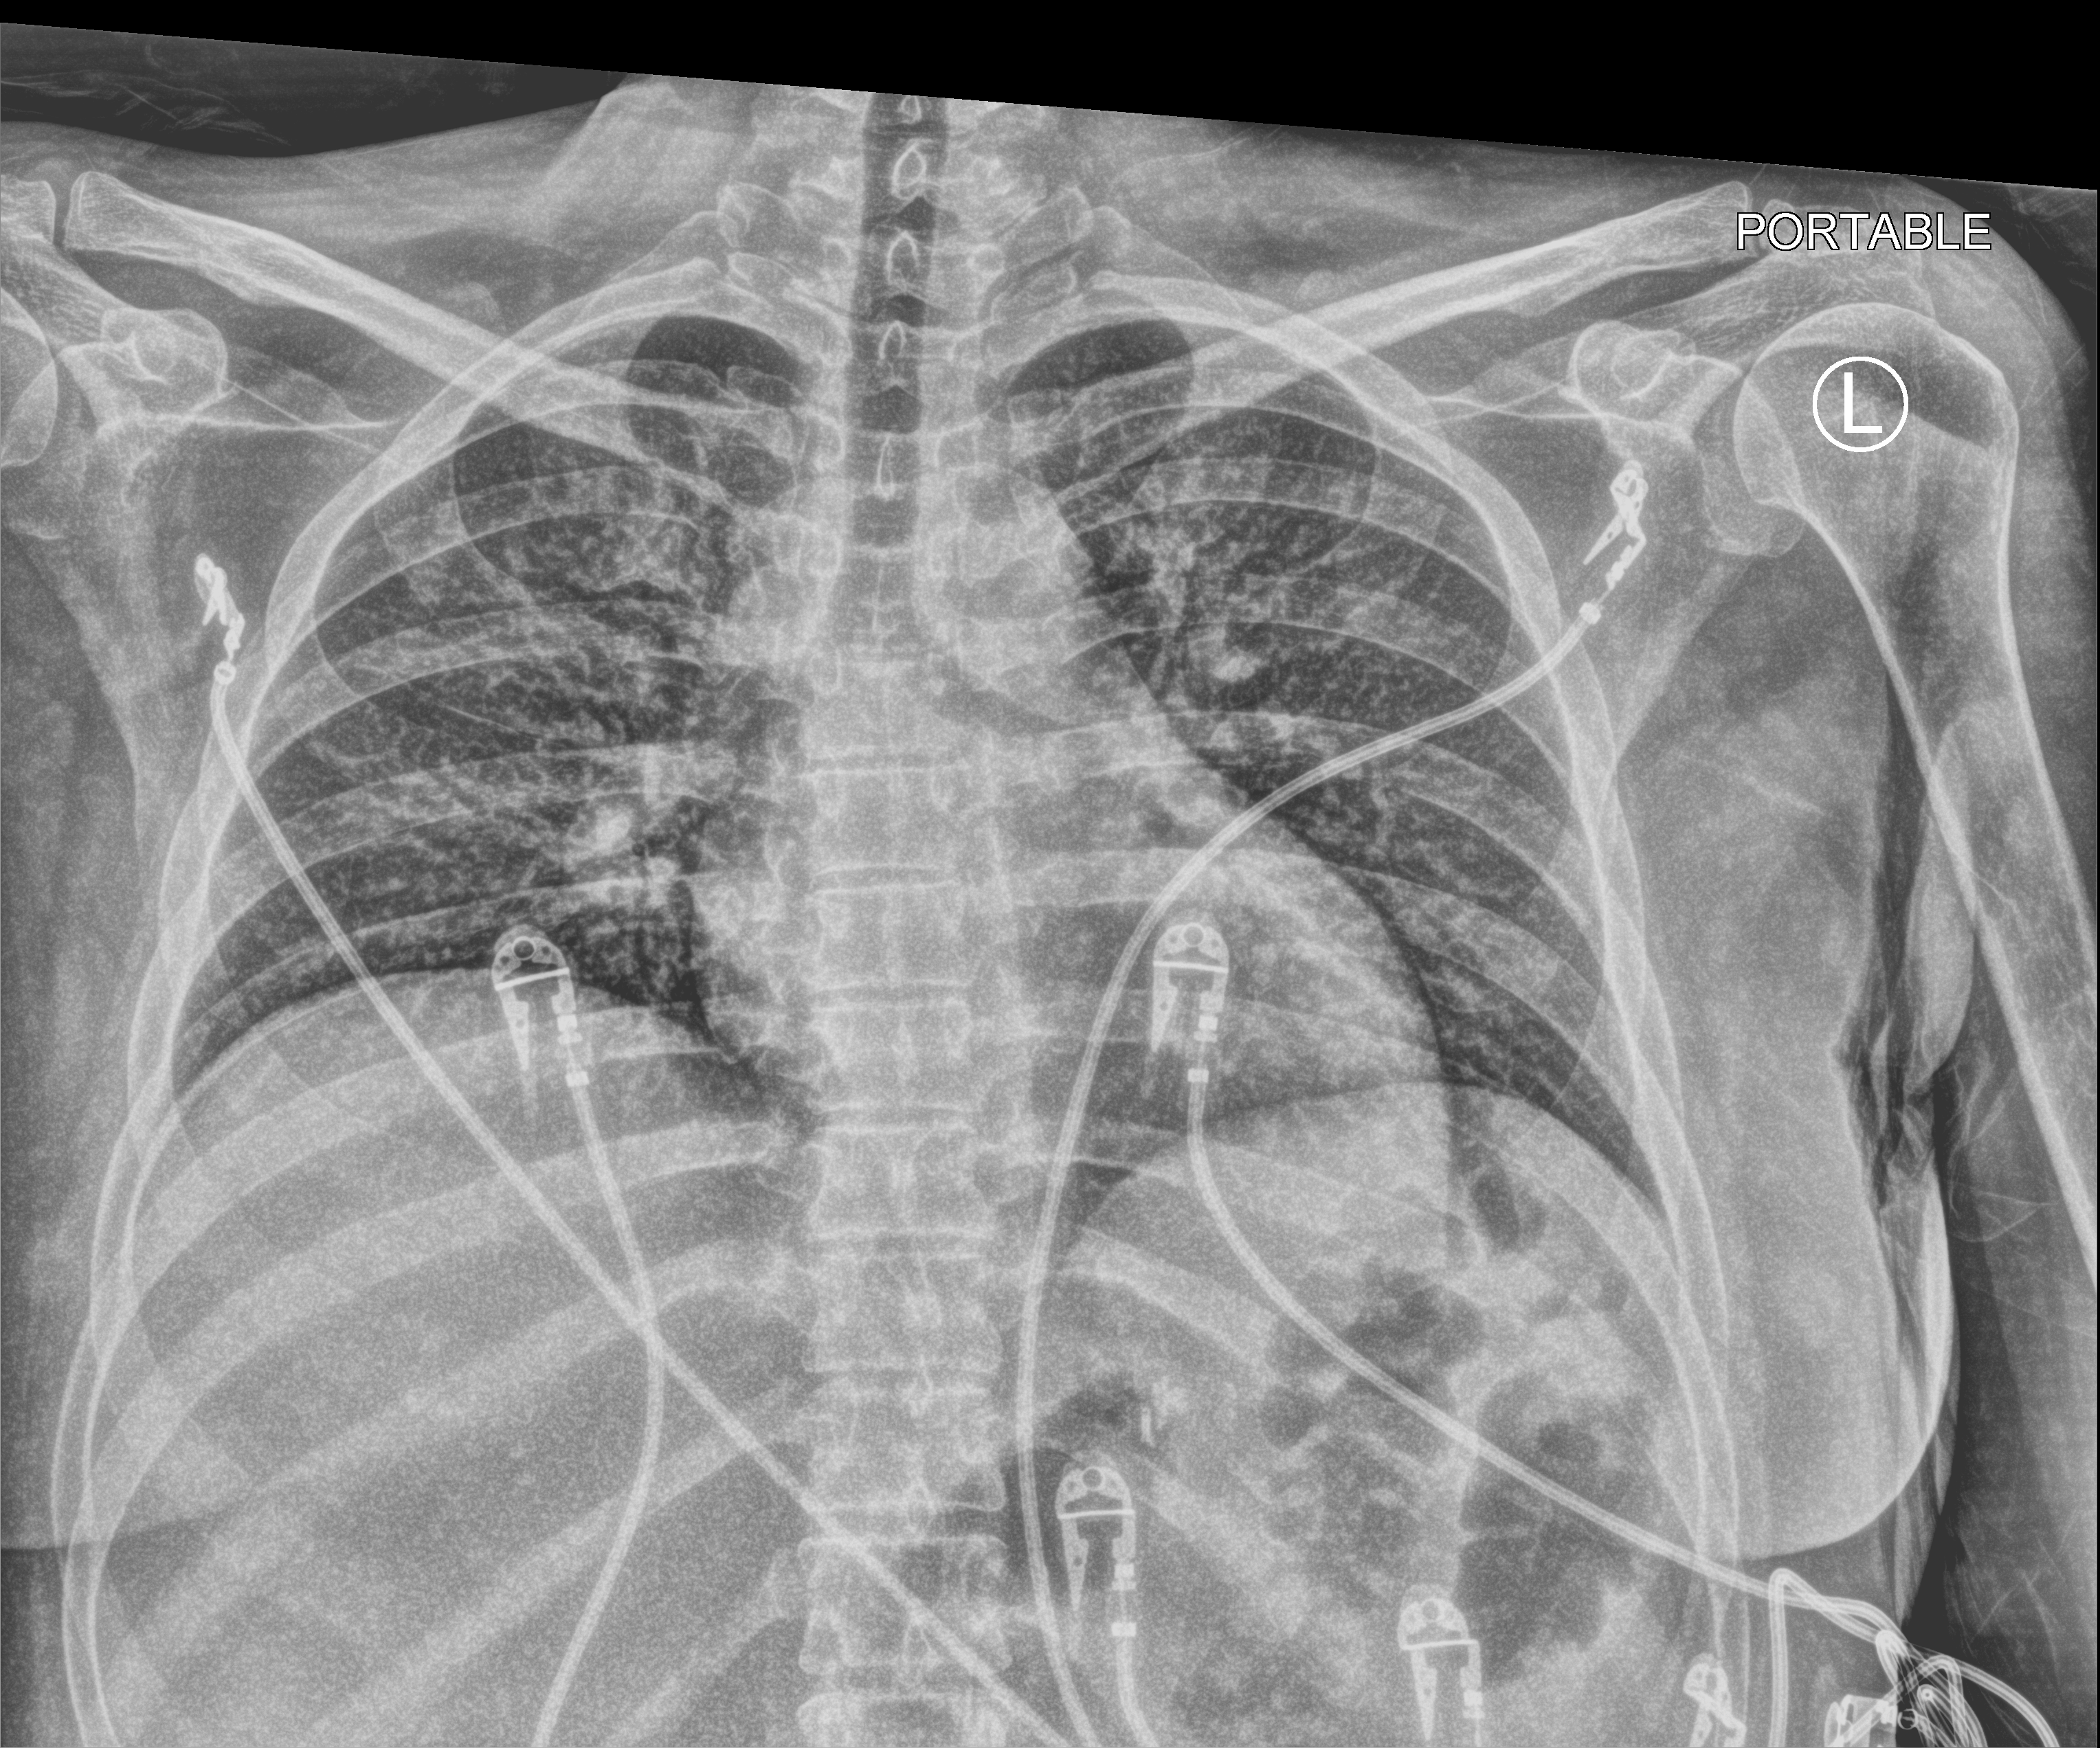
Bedside chest radiograph (computed radiography), anteroposterior (AP) projection. Female patient hospitalised with COVID-19, age 18–59 years.
Admission-level facts for this patient (not findings on this image; timing relative to this image not recorded):
- admitted to intensive care during this hospital stay: no
- mechanically ventilated during this hospital stay: no